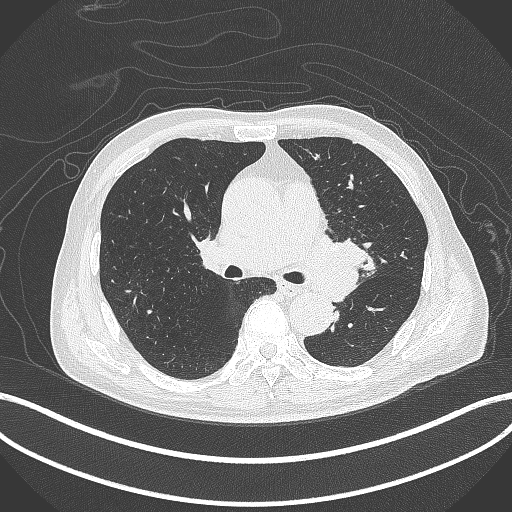
Chest CT, one axial slice; position 256 of 417 along the scan axis; lung window (W 1500 / L -600 HU); 1 mm slice thickness; 512 × 512 image matrix. Male patient, age 77 years. Case-level facts recorded for this patient, not image findings: clinical TNM (as recorded): T3 N1 M0.
Outlined on this slice (bounding box drawn by a radiologist):
- lung tumour (recorded histology: adenocarcinoma): bounding box <311,228,382,307> (left, top, right, bottom; pixels)